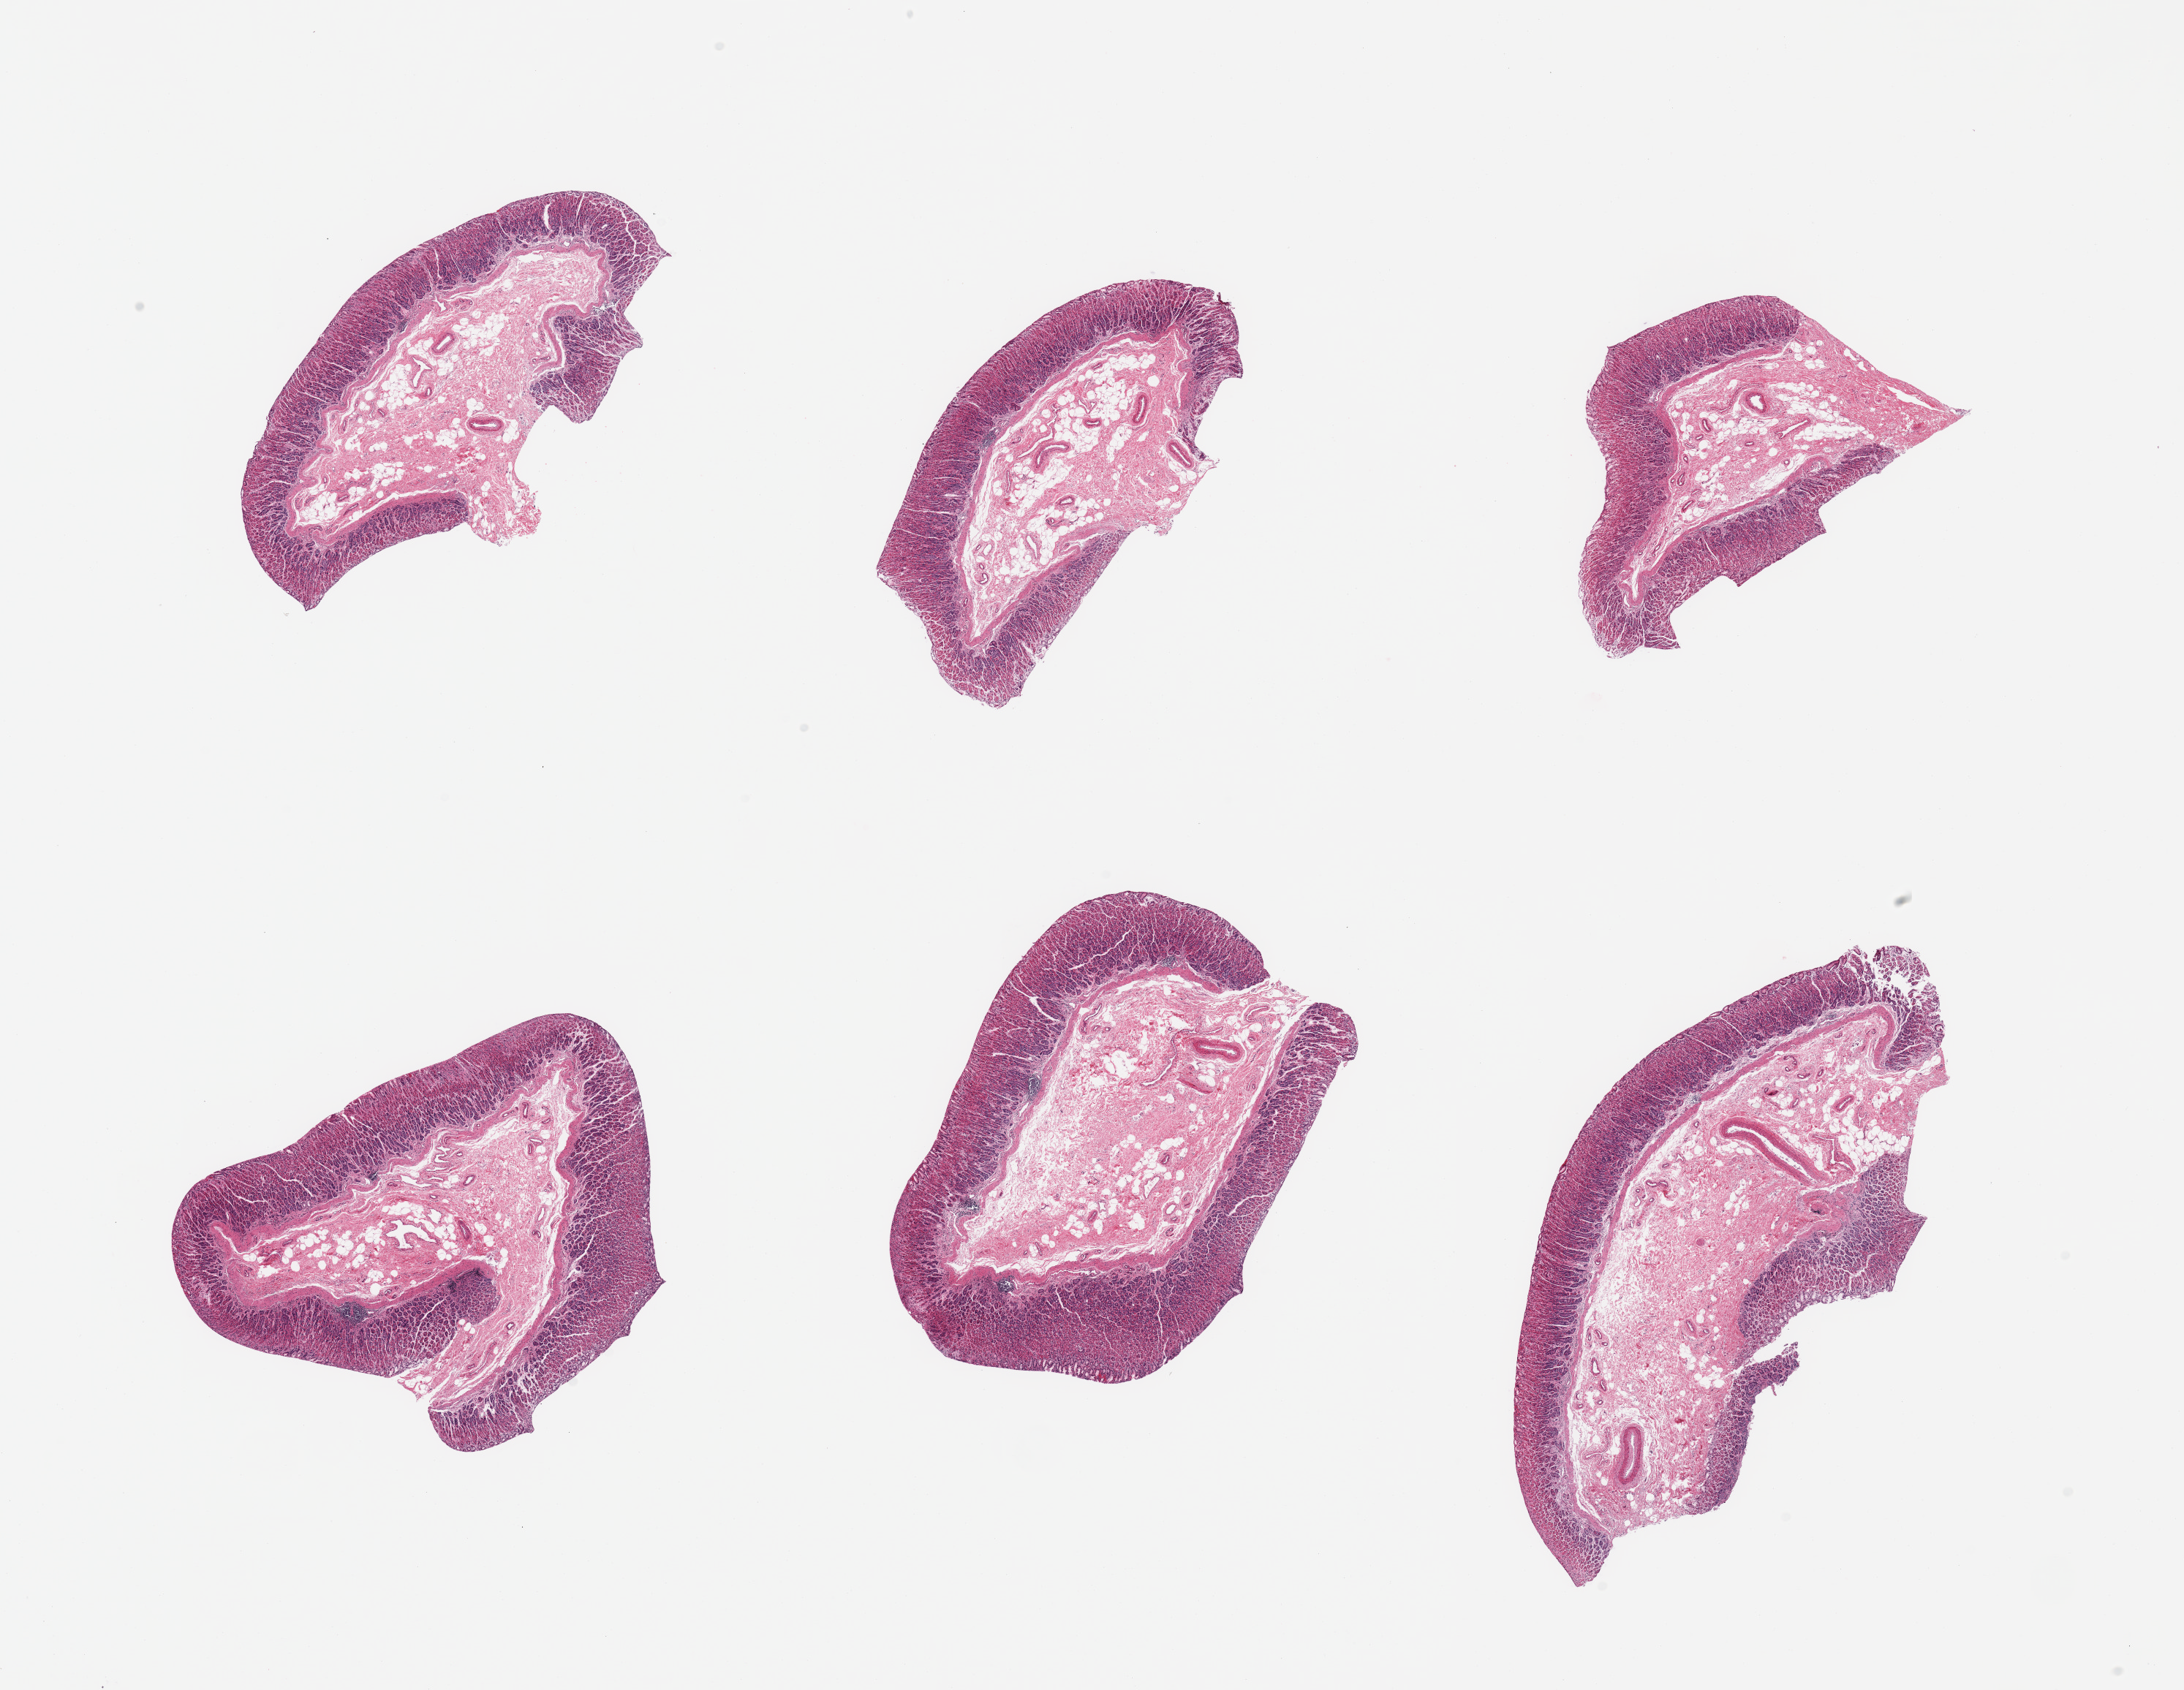
Haematoxylin and eosin whole-slide image, brightfield, shown as a low-resolution overview of the whole scanned area (about 23.6 x 18.3 mm, acquisition: 20x scan), PAXgene-fixed paraffin-embedded (PFPE) section, target tissue: stomach, tissue donor sample. Female donor.
Pathologist's review note for this sample: 6 pieces; mild autolysis of mucosa and submucosa.